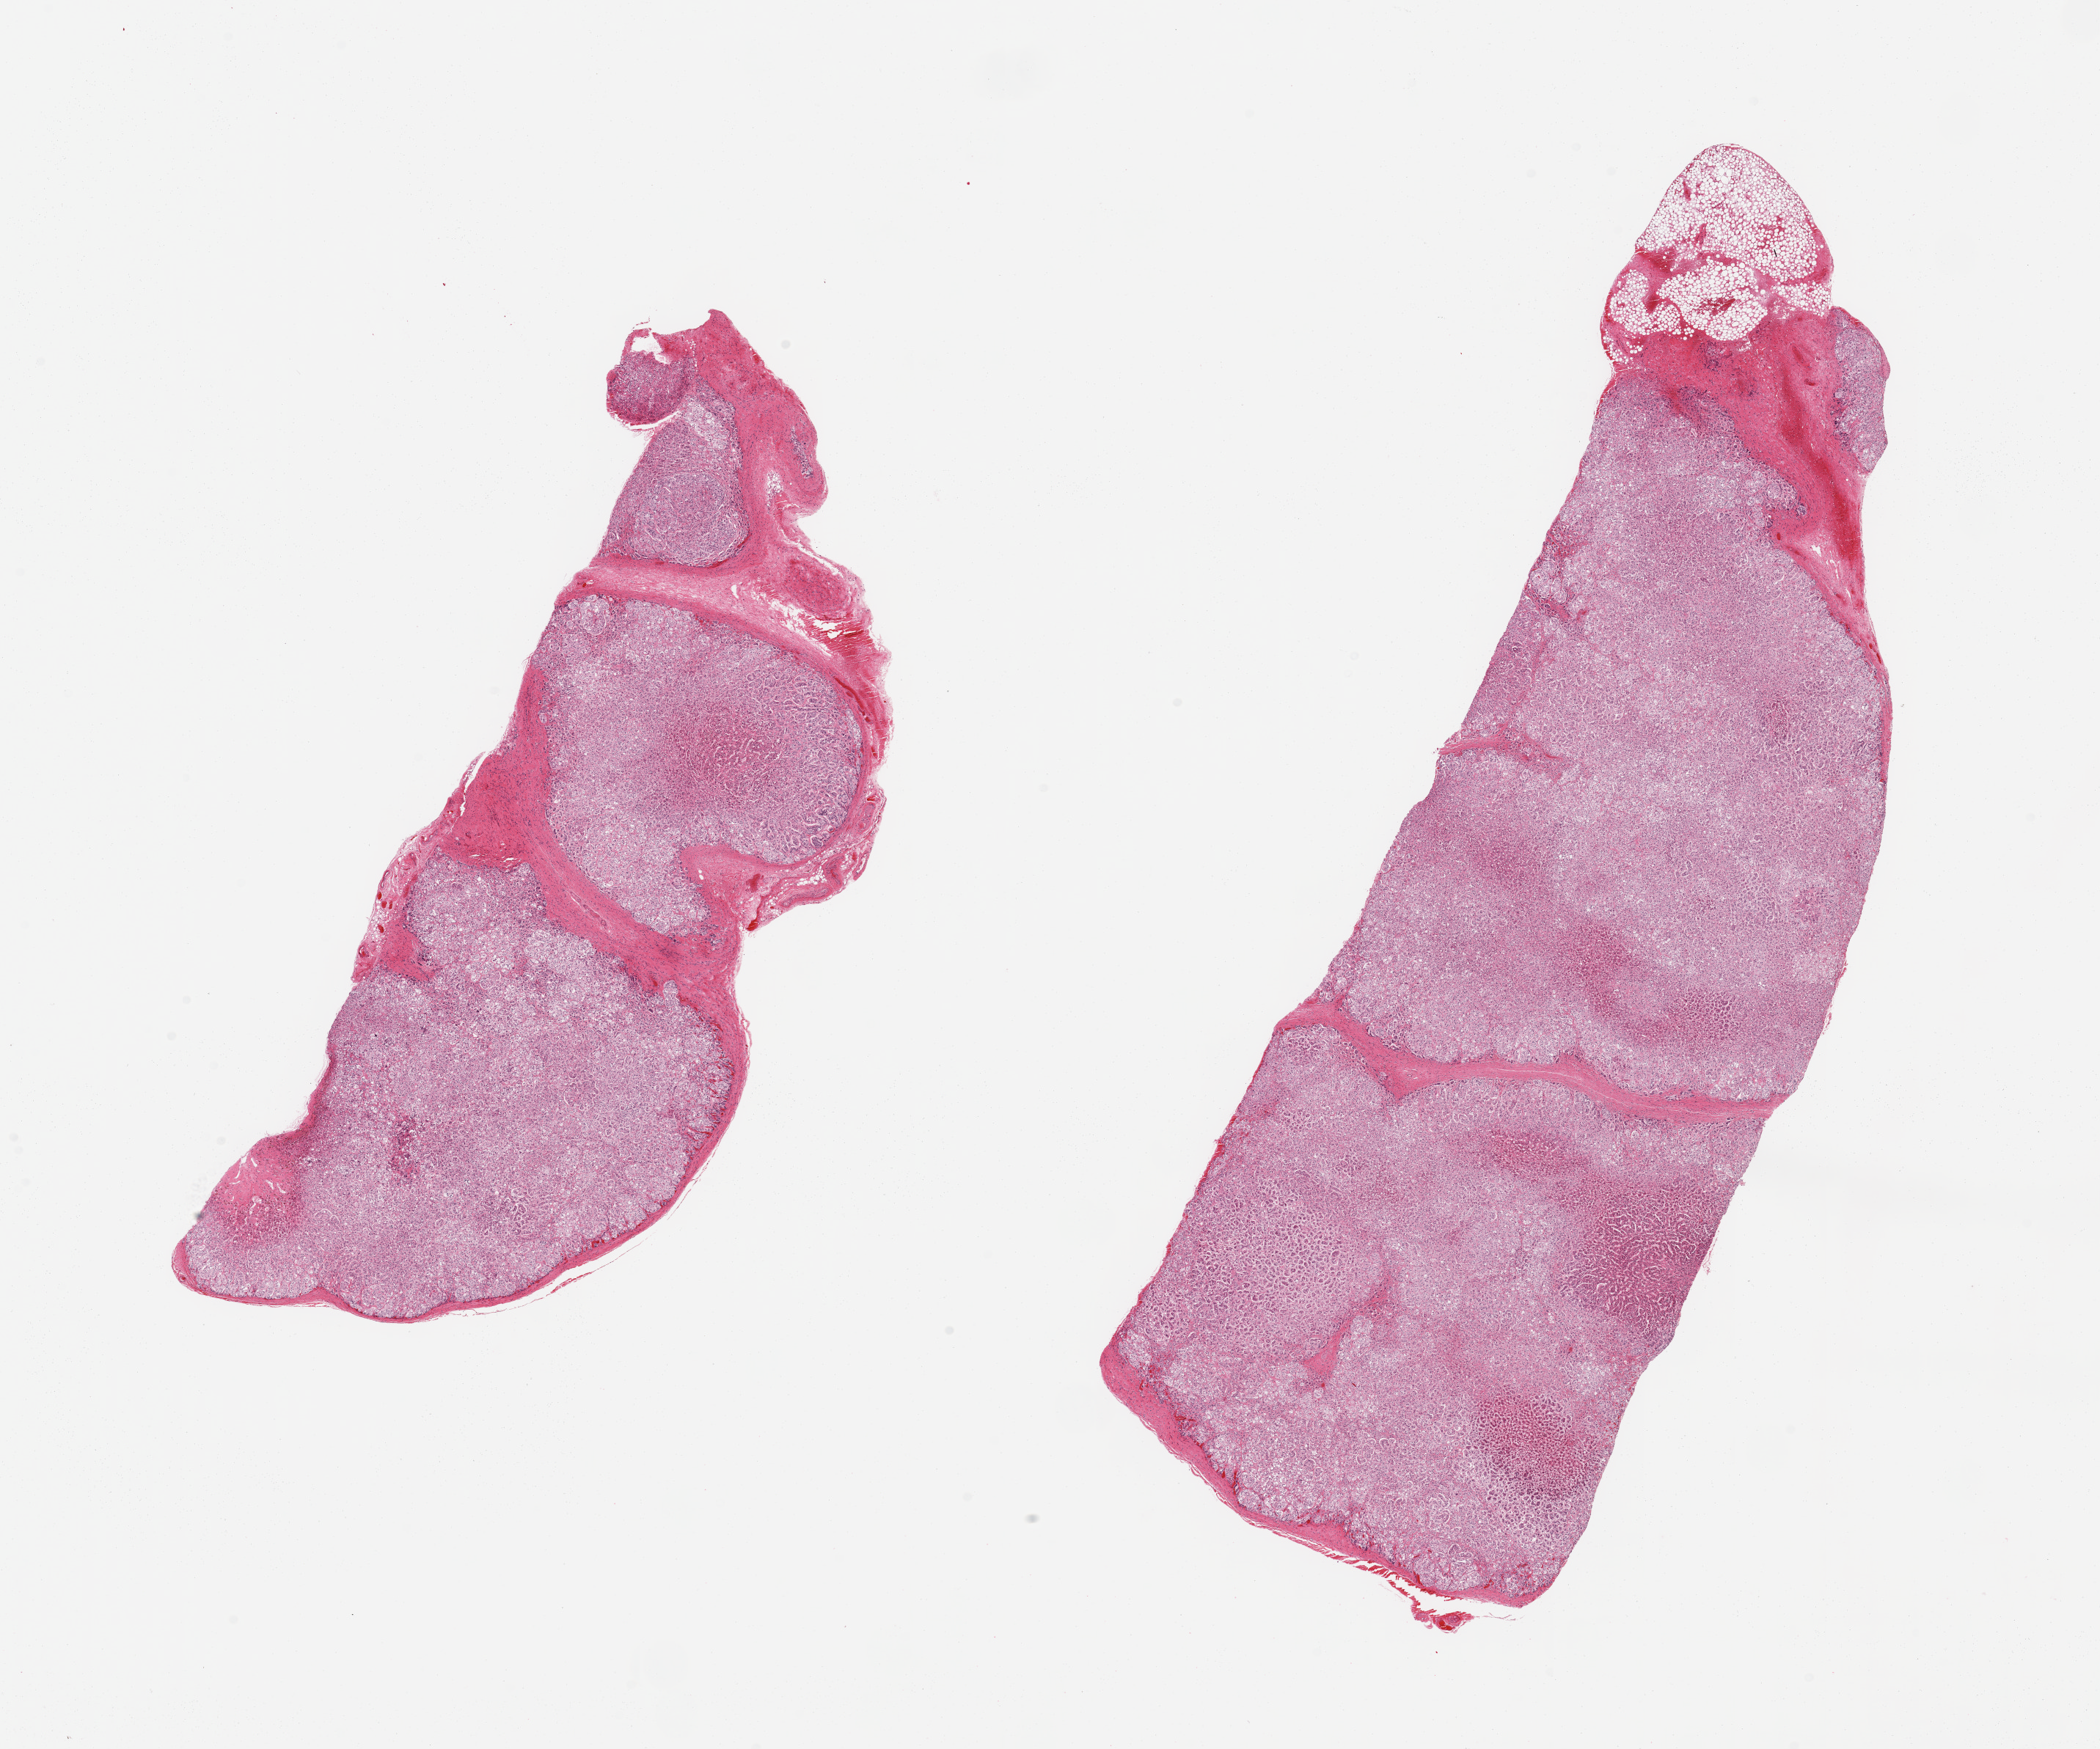
Hematoxylin and eosin (H&E) whole-slide image, whole scanned area (about 22.6 x 18.9 mm, slide scanned at 20x) shown as a low-resolution overview. PAXgene-fixed, paraffin-embedded tissue. Target tissue: adrenal gland. Donor tissue sample.
* review note (as recorded): 2 pieces; moderate to severe autolysis of adrenal cortex; fibrous septa; trace and 2% of external fat